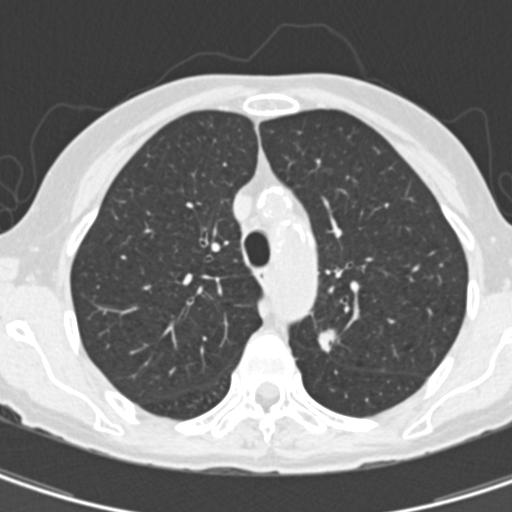
Axial slice from a low-dose chest CT screening exam, baseline annual screen, lung window (W 1500 / L -600 HU), standard (soft-tissue) reconstruction kernel (B30f), 512 × 512 image matrix, field of view 260 × 260 mm. Female participant, aged 67 years at enrolment. Current smoker at enrolment.
Expert reader's lesion annotation, bounding box <310,320,351,371> (left, top, right, bottom; pixels). The exam's reader record, not a measurement of the box and not confirmed to be the same lesion: non-calcified nodule or mass ≥4 mm, left upper lobe, 11 × 8 mm, spiculated (stellate) margins, soft tissue attenuation. Official screen result: positive, change unspecified: nodule(s) >= 4 mm or enlarging nodule(s), mass(es), or other non-specific abnormalities suspicious for lung cancer. Later outcome: lung cancer diagnosed 73 days after this screen — adenocarcinoma, NOS, left upper lobe, poorly differentiated (G3), stage IA (AJCC 6th edition), 13 mm at pathology.